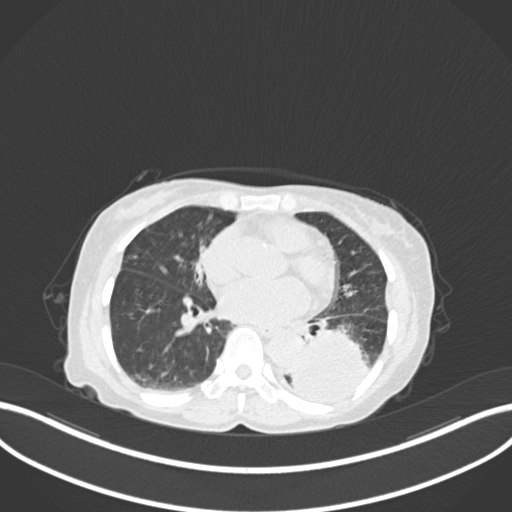
Chest CT, one axial slice; reconstruction kernel B30f; lung window (W 1500 / L -600 HU); 512 × 512 image matrix. Female patient, age 78 years. From the clinical record (not read from this slice): clinical TNM (as recorded): T3 N0 M1.
Structures marked on this image (rectangle marked by the reading radiologist):
- lung tumour (recorded histology: squamous cell carcinoma): bounding box <290,330,372,409> (left, top, right, bottom; pixels)